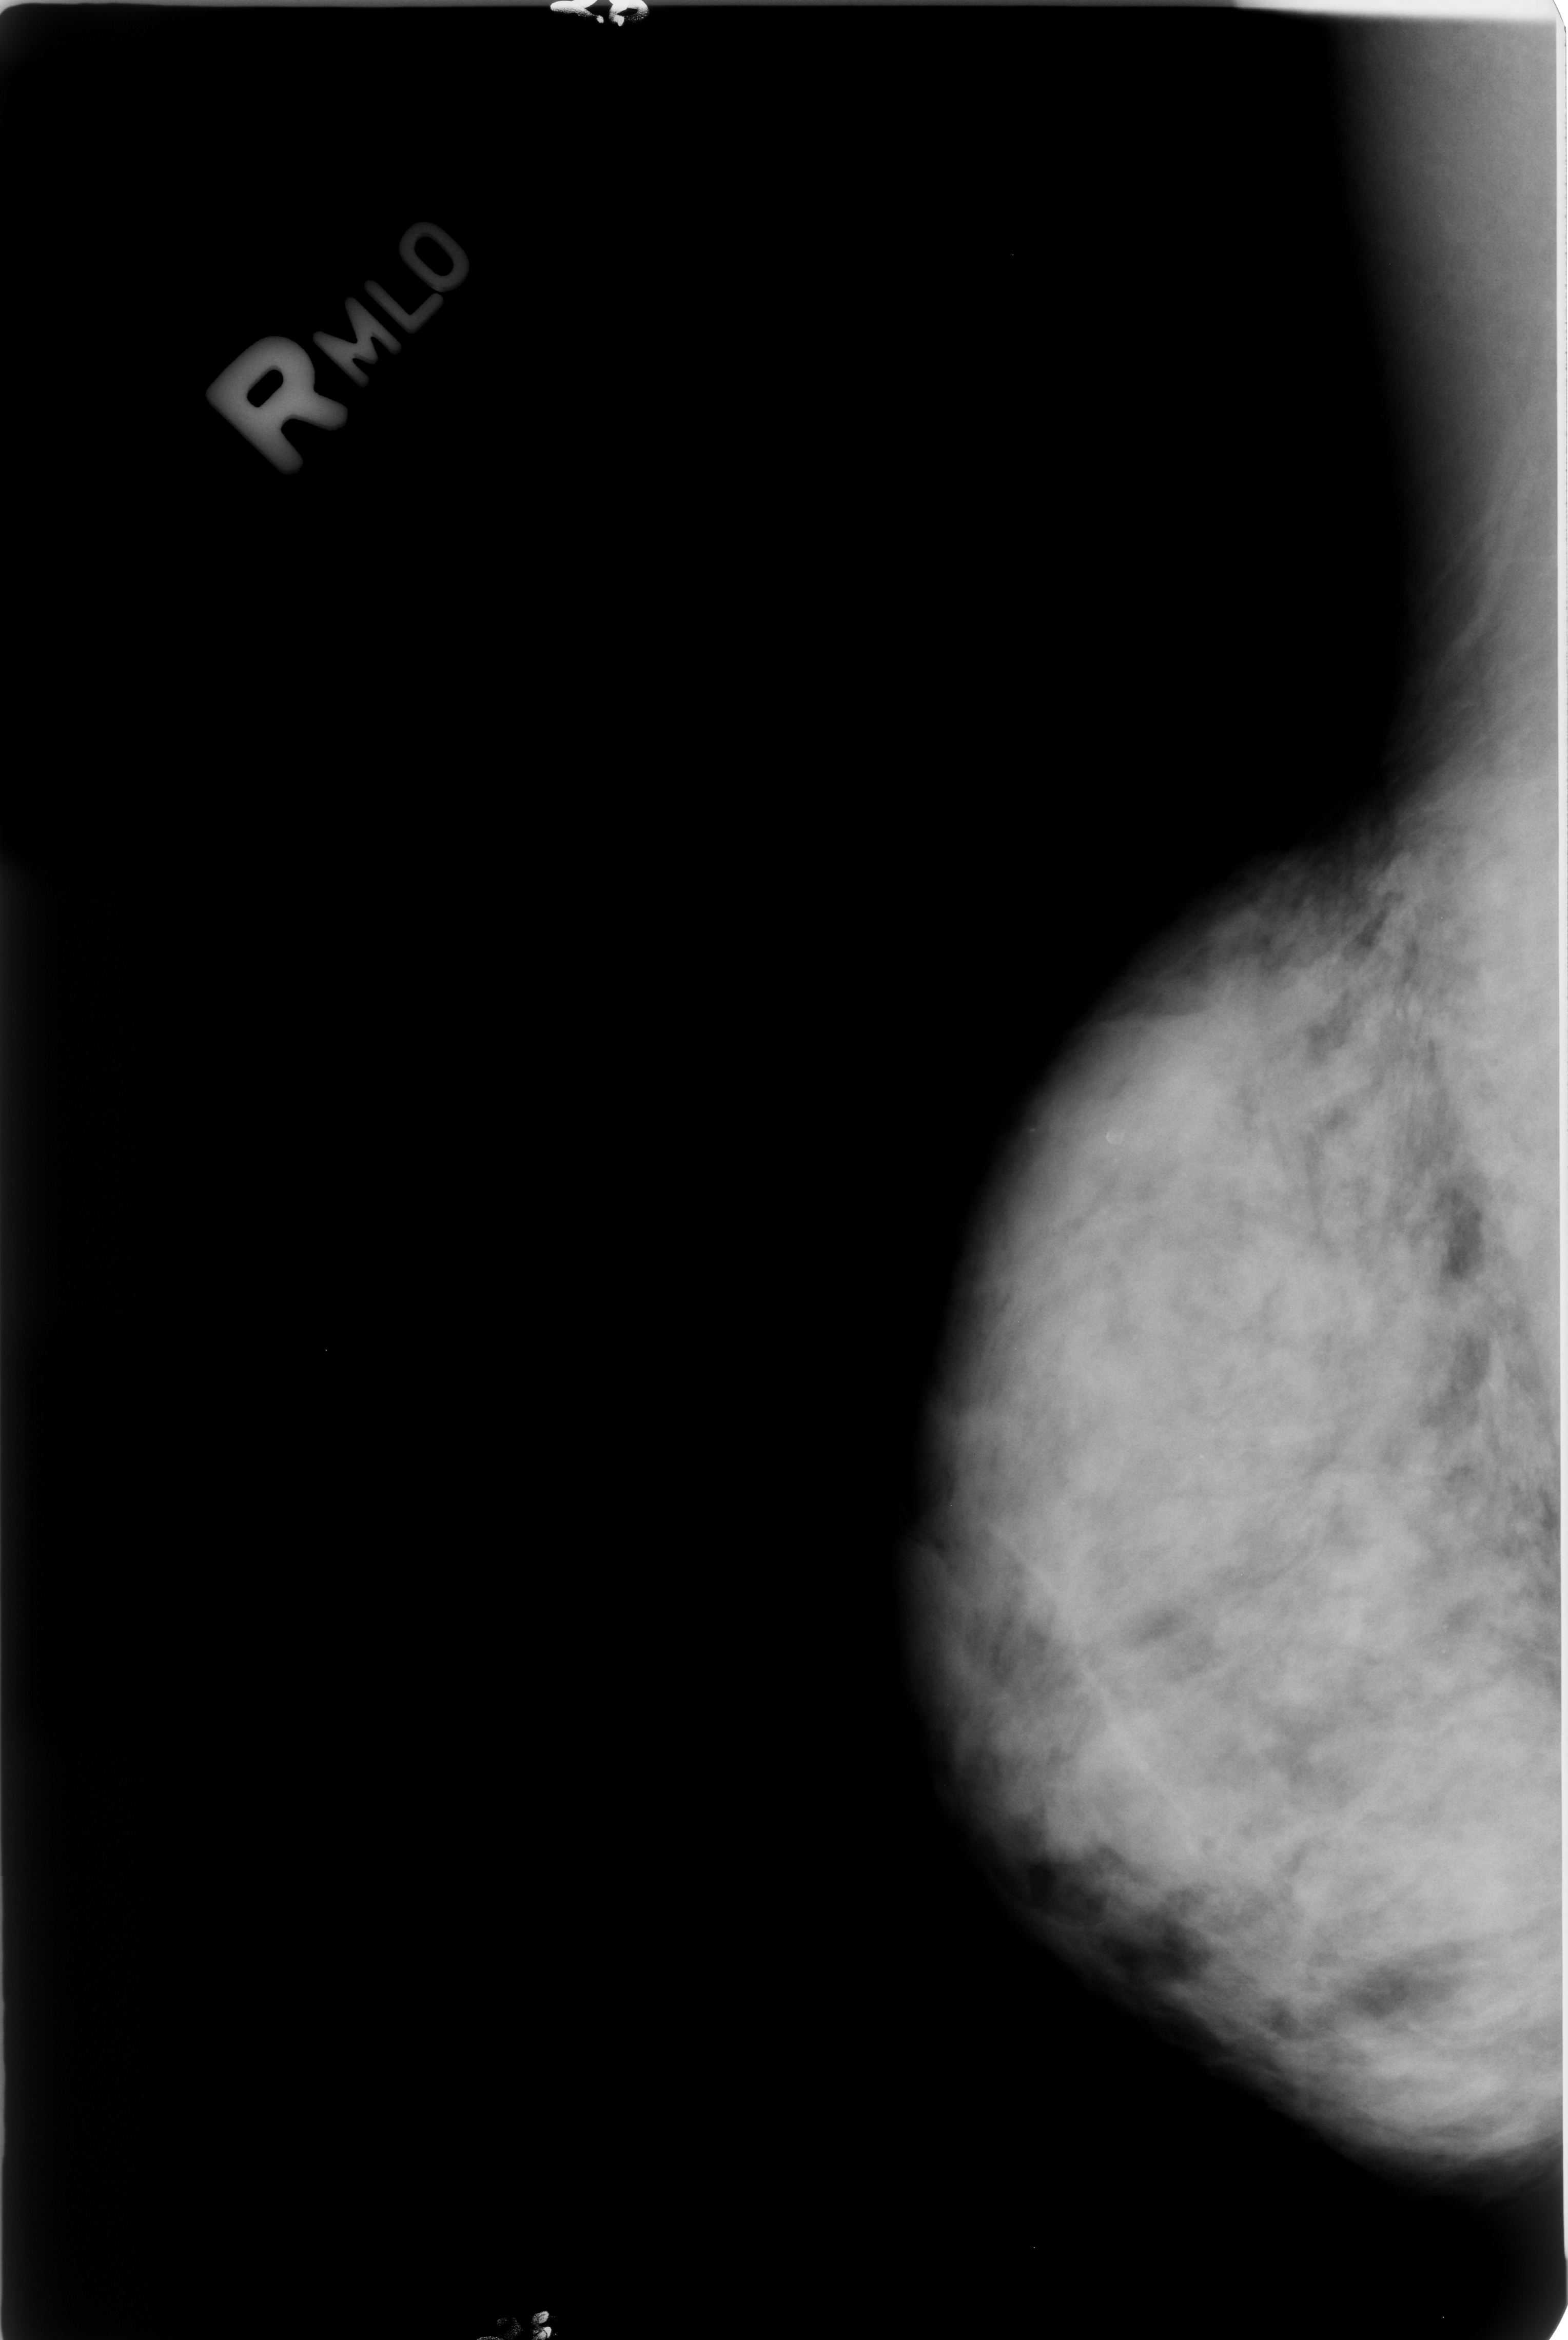
Scanned film-screen mammogram; right breast; mediolateral oblique (MLO) view; breast composition: extremely dense (BI-RADS density category 4 of 4); 1568 × 2340 image matrix.
Expert-marked regions of interest on this image (one box per marked abnormality):
- calcifications, morphology lucent center; BI-RADS assessment category 2; subtlety rating 3 on a 1 (subtle) to 5 (obvious) scale; outcome (as recorded, no biopsy): benign without callback (not worked up further): bounding box (x1, y1, x2, y2) in pixels: (1083, 1124, 1122, 1167)